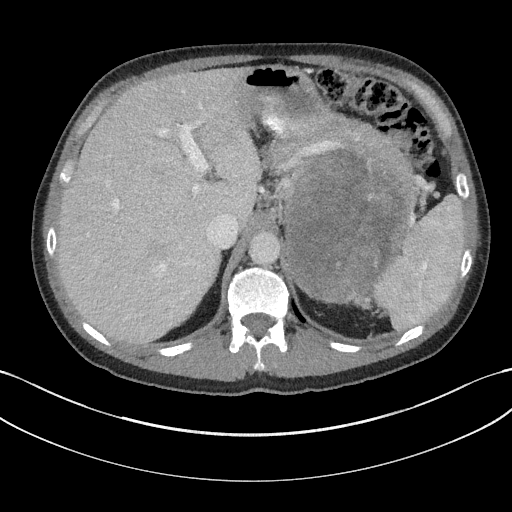
Contrast-enhanced abdominal CT, one axial slice. Position 122 of 147 along the scan axis. 100 kVp. Soft-tissue window (W 400 / L 40 HU). 512 × 512 image matrix, field of view 384 × 384 mm. Male patient, age 58 years. Case-level facts recorded for this patient, not image findings: diagnosis: adrenocortical carcinoma; tumour side: left adrenal; tumour size at pathology: 22 cm; Ki-67 index: 26 %; stage (as recorded): 2.
Structures marked on this image (semi-automatically segmented with operator editing):
- mass: bounding box (x1, y1, x2, y2) in pixels: (287, 150, 408, 302)